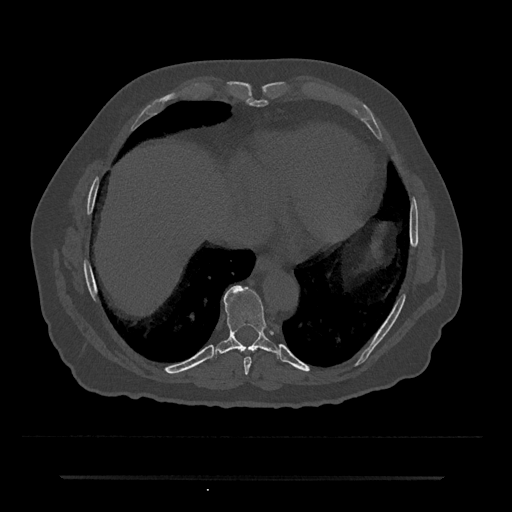
CT including the spine, one axial slice. Position 289 of 797 along the scan axis. 120 kVp. Bone window (W 1800 / L 400 HU). 0.5 mm slice thickness. 512 × 512 image matrix. Patient: male, 69 years. Case-level facts recorded for this patient, not image findings: primary cancer: prostate.
Structures marked on this image (semi-automatically segmented with operator editing):
- T8 vertebra: bounding box [x1, y1, x2, y2] px = [244, 357, 252, 375]
- T9 vertebra: [215, 285, 279, 355]